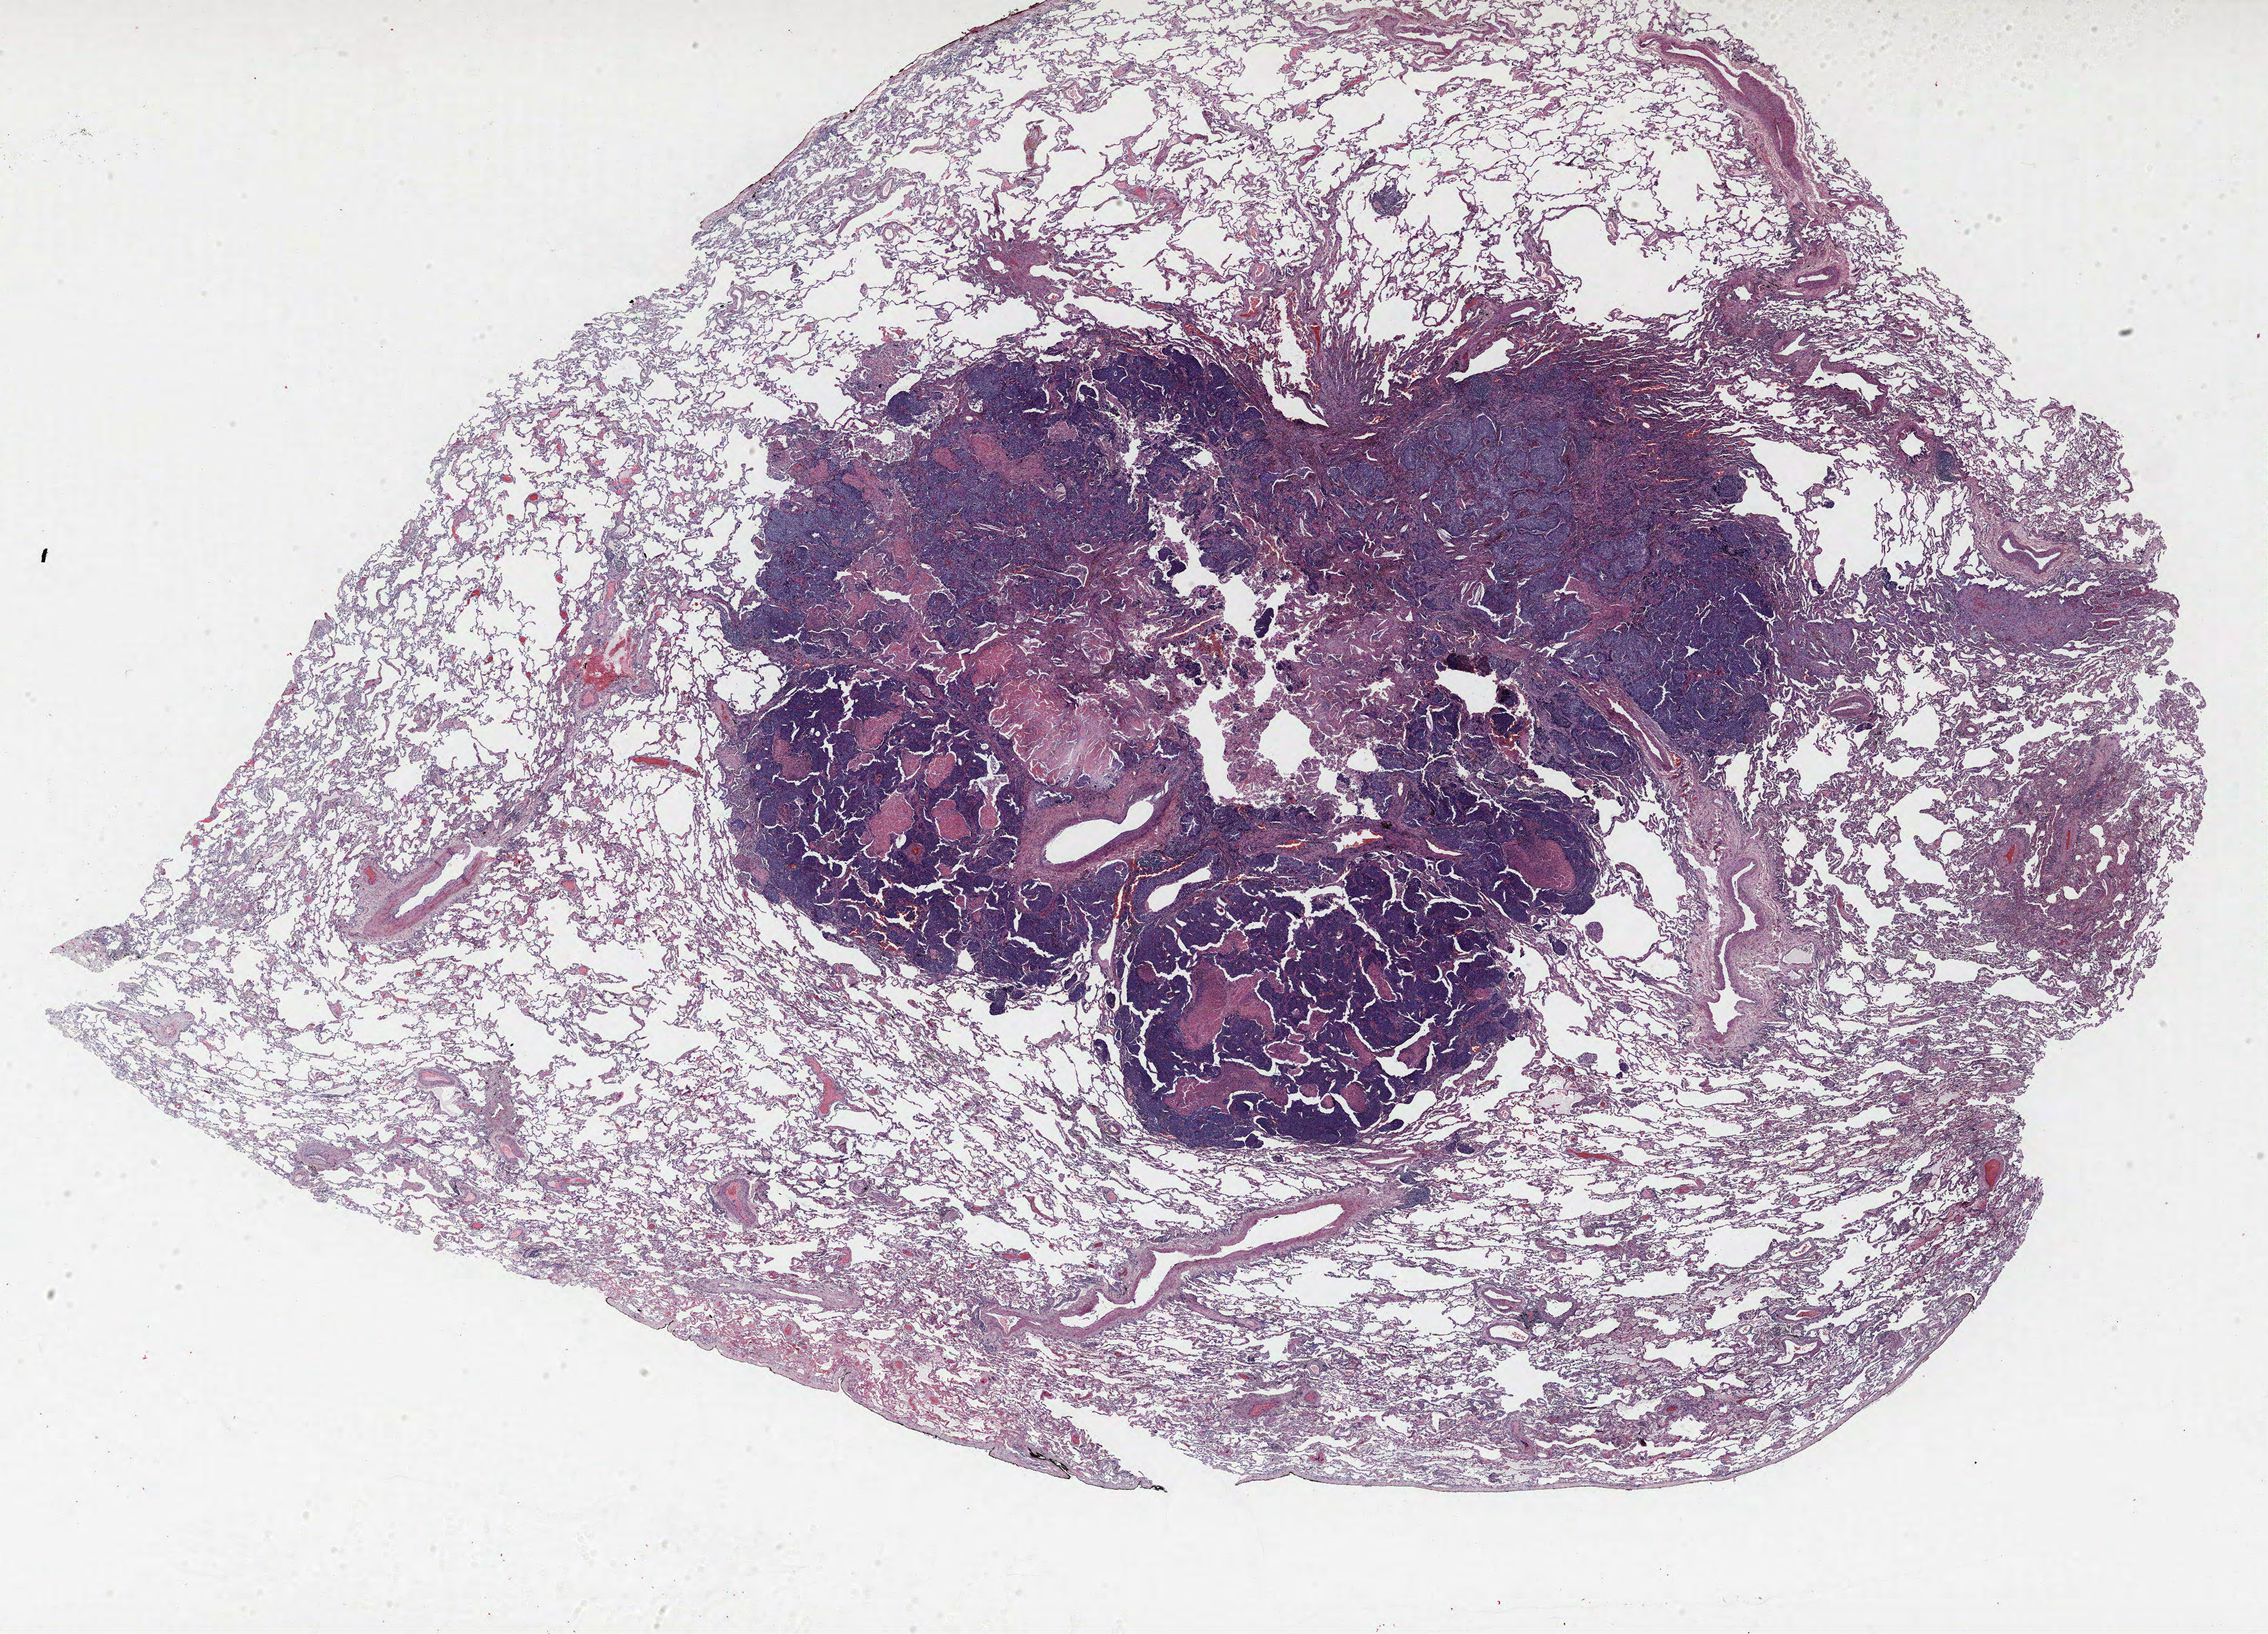
Whole-slide histology image, Hematoxylin and eosin (H&E) stained — low-resolution overview of the scanned area, about 29.0 x 20.9 mm; formalin-fixed paraffin-embedded (FFPE) section; lung. Male, age 69 at enrolment. Former smoker at enrolment. Grade: poorly differentiated (G3).
- stage (AJCC 6th edition): IV
- primary tumour location (clinical record): left upper lobe
- tumour size (pathology): 18 mm
- participant's lung-cancer diagnosis: Squamous cell carcinoma, NOS